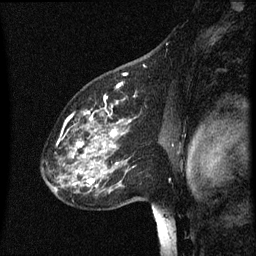
Breast MRI (dynamic contrast-enhanced), one sagittal slice. Position 42 of 60 along the scan axis. Dynamic contrast-enhanced series, image 2 of 3 at this slice position (ordered by acquisition). 1.5 T. TE 4.2 ms, TR 8 ms. 2 mm slice thickness. 256 × 256 image matrix, field of view 200 × 200 mm. Patient: female, 60 years.
Structures marked on this image (semi-automatic segmentation, software-assisted and operator-edited):
- analysis volume of interest (the breast-tissue region the enhancement analysis was run in; not a lesion): bounding box [x1, y1, x2, y2] px = [49, 96, 137, 197]
- tumour enhancement mask (voxels above the 70 % enhancement threshold inside the analysis volume of interest): [61, 100, 135, 187]